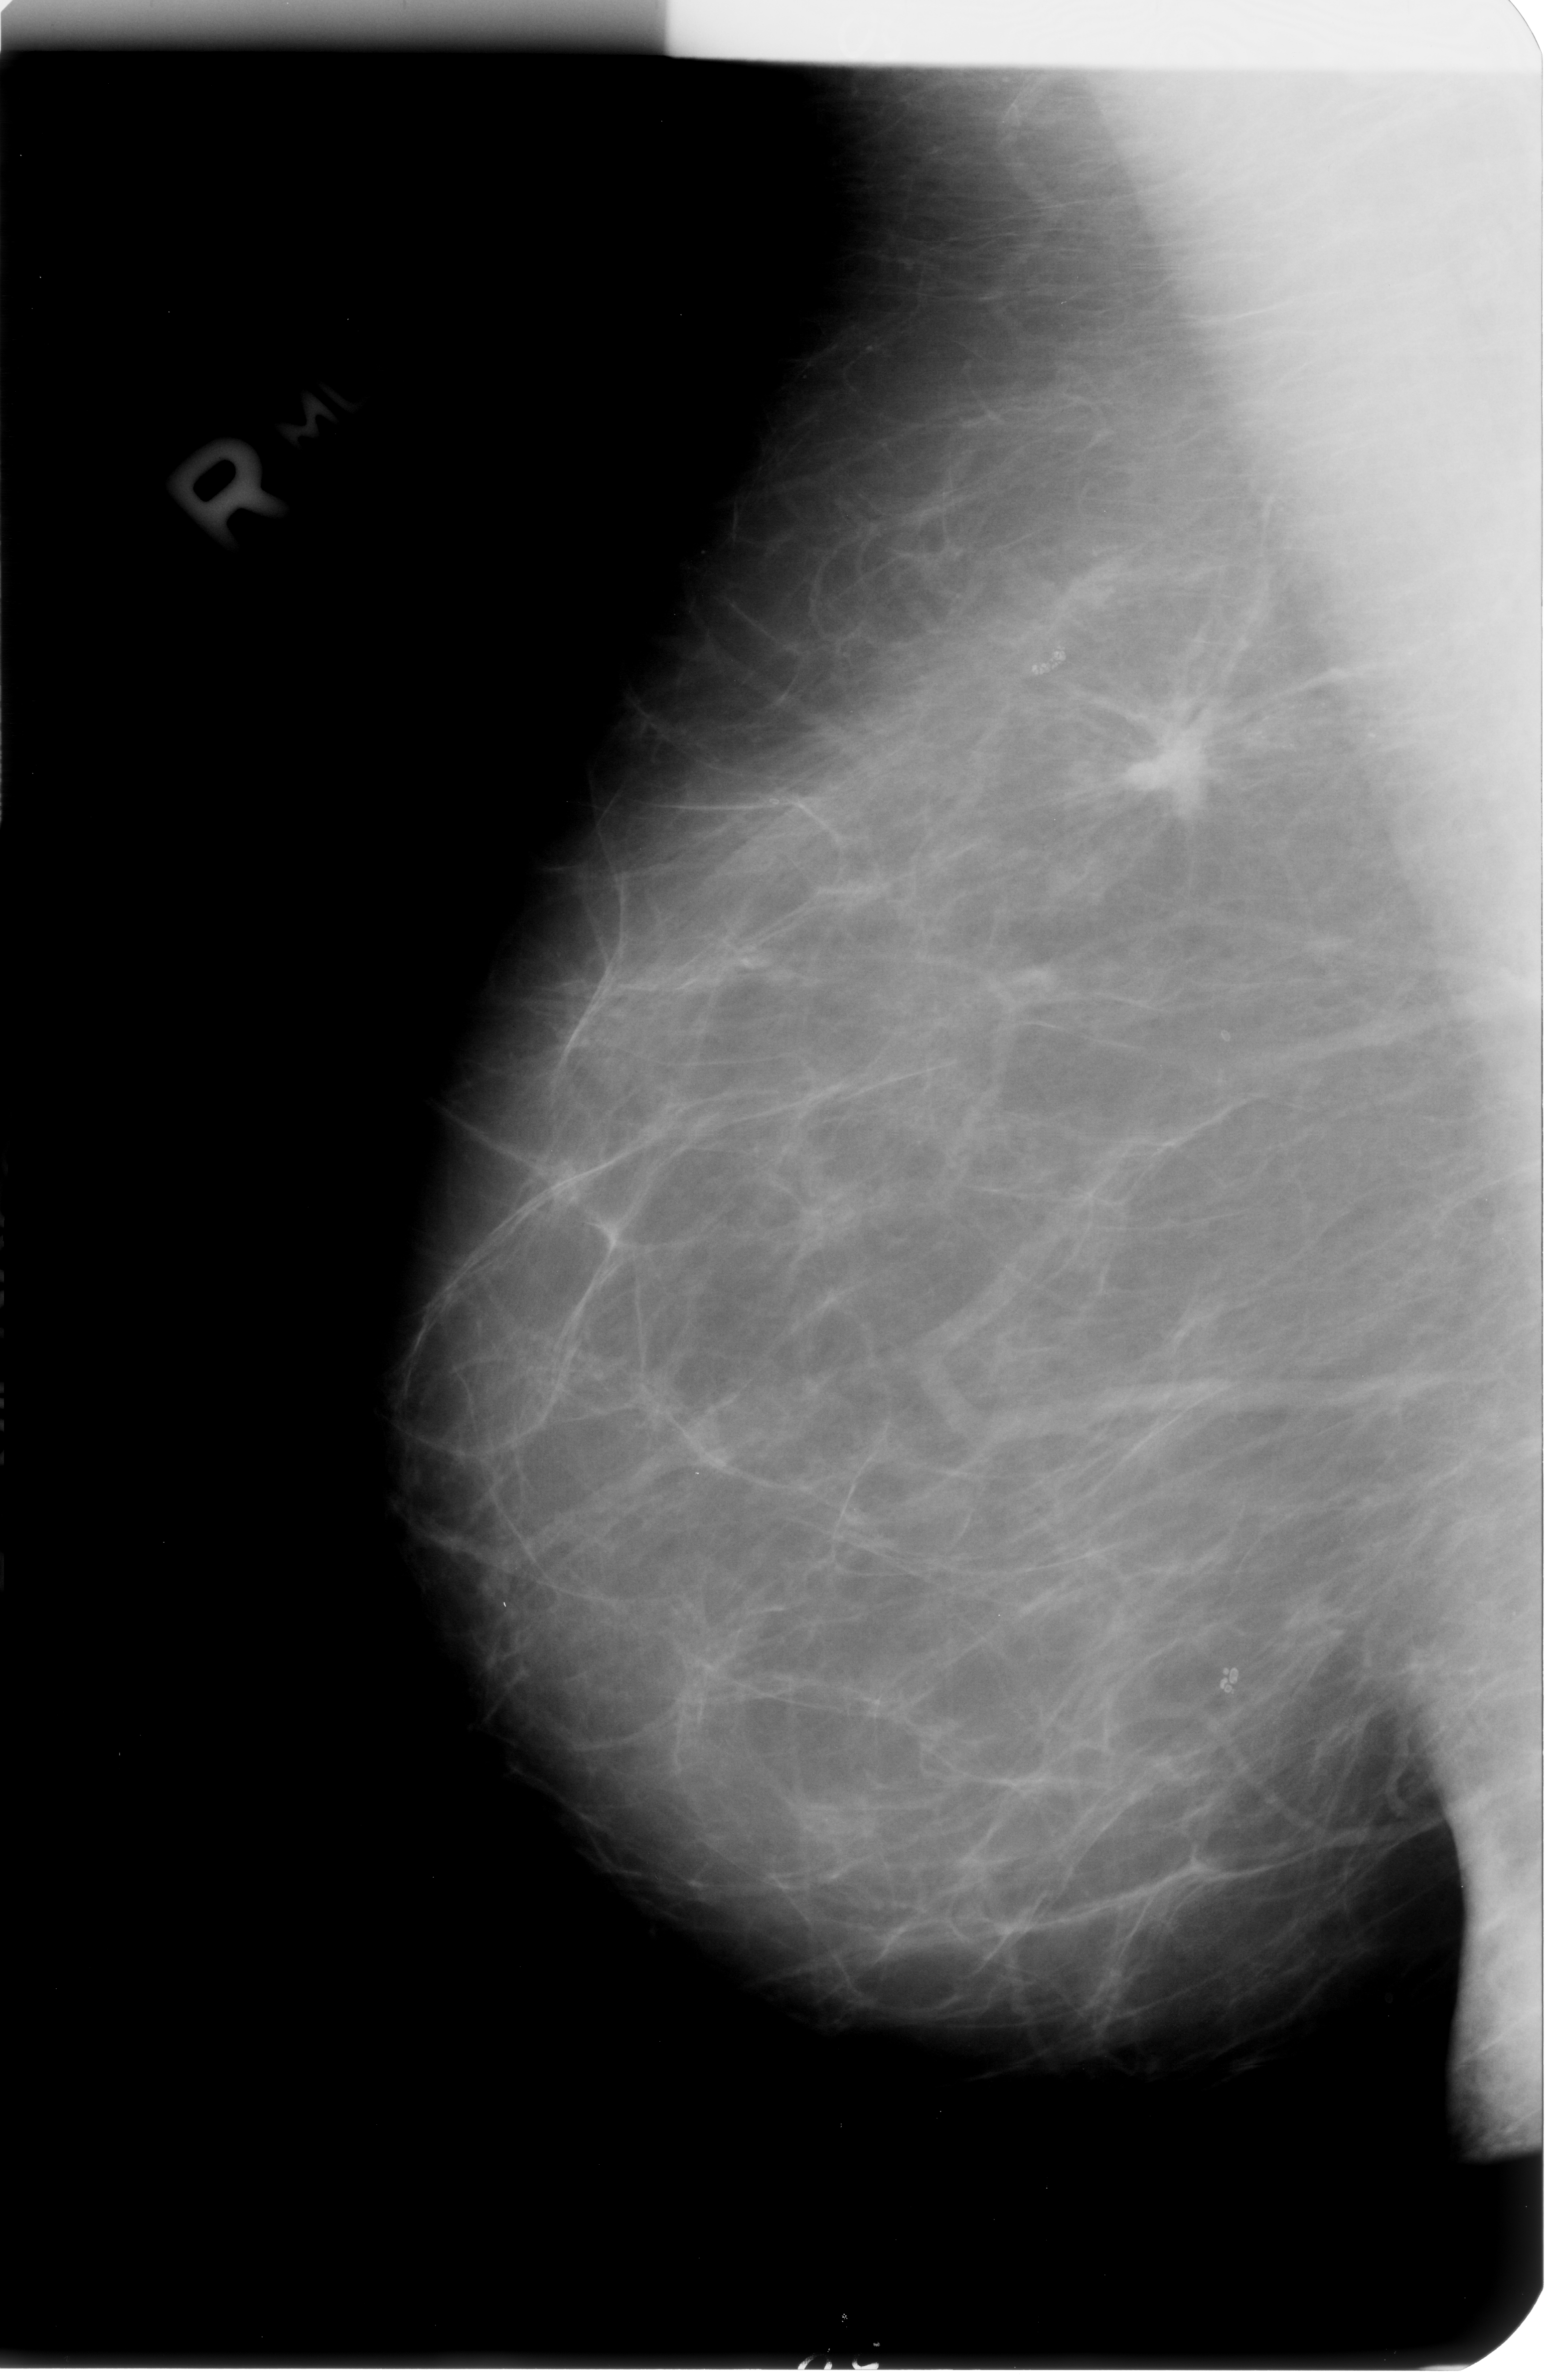
Mammogram (digitized film). Right breast. MLO view. Breast composition: almost entirely fatty (BI-RADS density category 1 of 4). 1551 × 2380 image matrix.
Marked abnormalities (boxes around the expert regions of interest):
- Finding 1 of 3: calcifications, morphology fine linear branching, distribution clustered / linear; BI-RADS assessment category 5; subtlety rating 4 on a 1 (subtle) to 5 (obvious) scale; pathology (as recorded): malignant: bounding box (x1, y1, x2, y2) in pixels: (1060, 586, 1301, 846)
- Finding 2 of 3: calcifications, morphology fine linear branching, distribution clustered / linear; BI-RADS assessment category 5; pathology result (as recorded, not read from the image): malignant: (1267, 729, 1301, 770)
- Finding 3 of 3: calcifications, morphology fine linear branching, distribution clustered / linear; BI-RADS assessment category 5; pathology (as recorded): malignant: (1351, 717, 1389, 766)